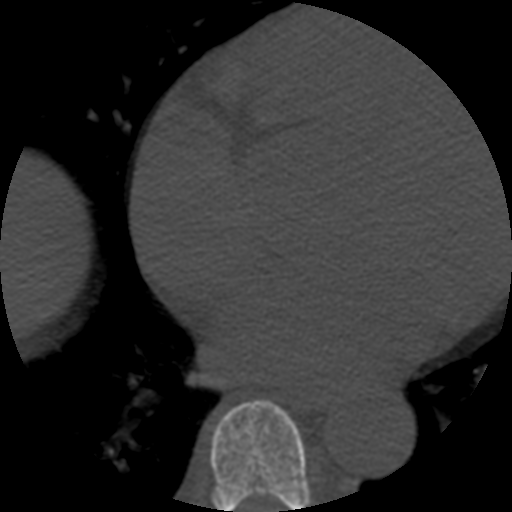
CT including the spine, one axial slice; slice 332 of 508 in the series (ordered by position); reconstruction kernel STANDARD; 120 kVp; bone window (W 1800 / L 400 HU); 1.25 mm slice thickness; 512 × 512 image matrix, field of view 160 × 160 mm. Patient age 57 years. From the clinical record (not read from this slice): primary cancer: prostate.
Structures marked on this image (semi-automatic segmentation, software-assisted and operator-edited):
- T7 vertebra: box from (x=210, y=400) to (x=311, y=512) px